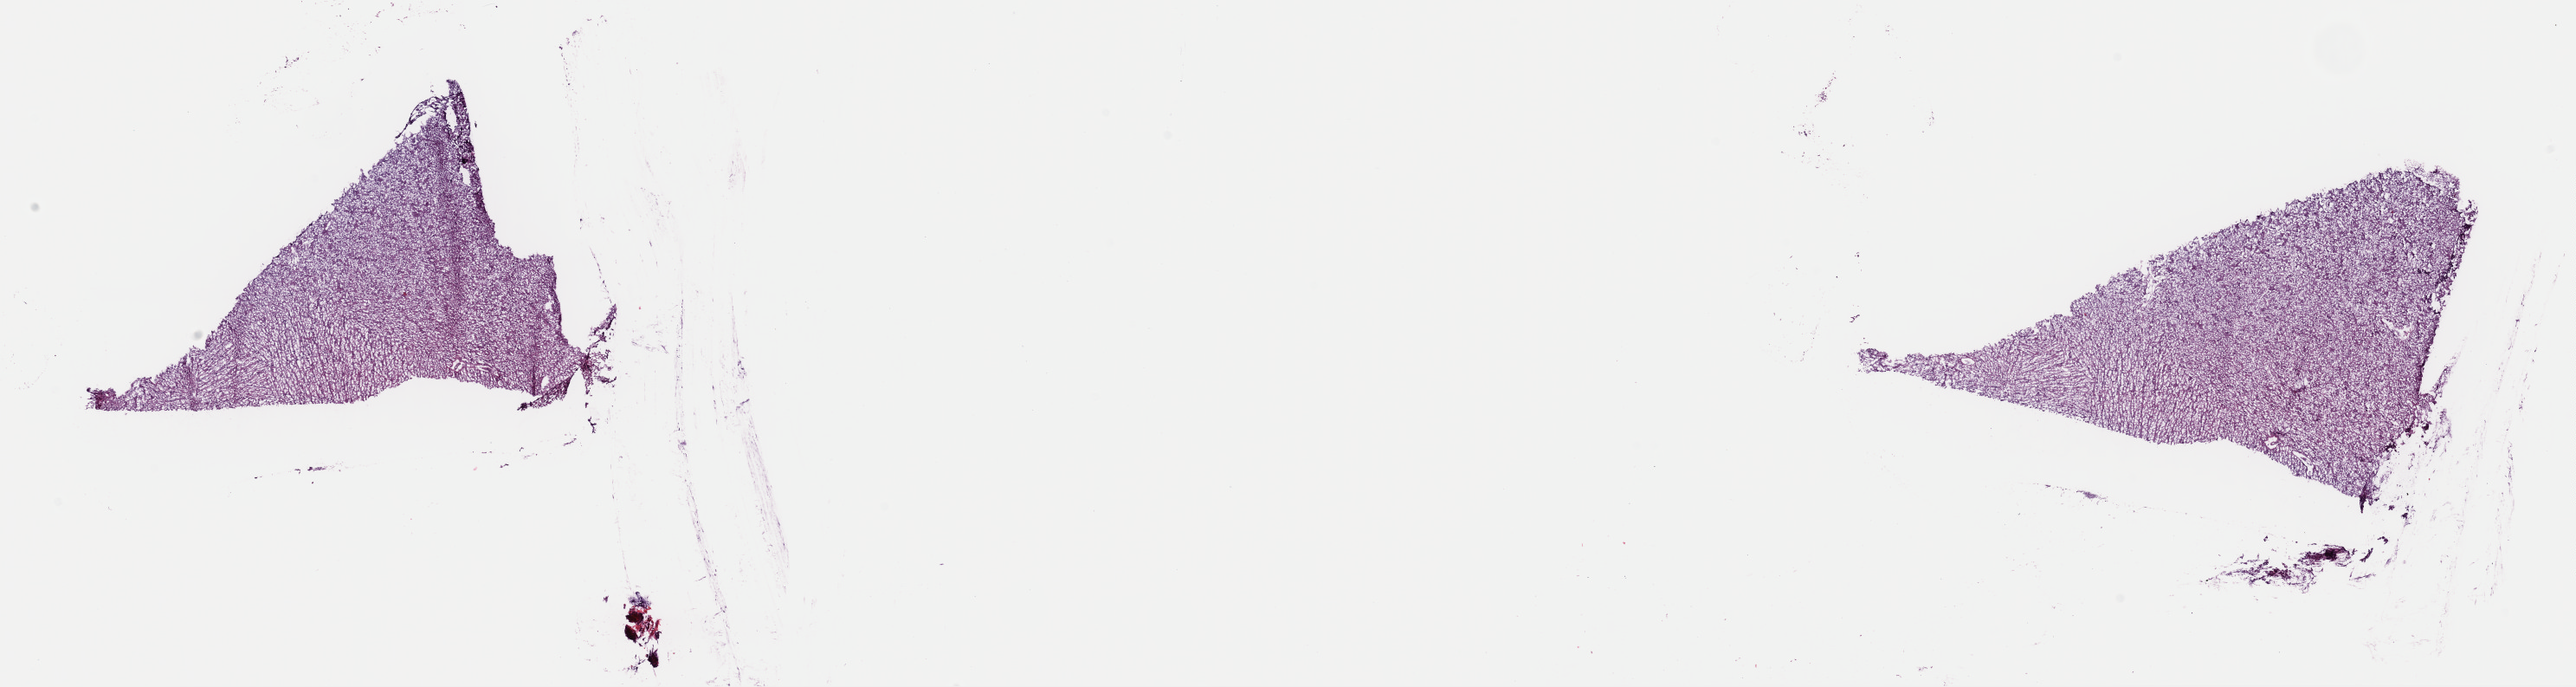
Whole-slide histology image, Hematoxylin and eosin (H&E) stained, low-resolution overview of the scanned area, about 23.5 x 6.3 mm, frozen section, primary tumour sample from the brain. Patient: female, age at initial diagnosis 45 years. Histologic grade: G2 (moderately differentiated). Pathologist review of this section (percent, as recorded): tumour cells 50%, tumour nuclei 80%, normal cells 10%, stromal cells 40%, necrosis 0%. Infiltration values recorded for this section: lymphocyte infiltration 0%, monocyte infiltration 0%, neutrophil infiltration 0%.
• laterality: left
• pathologic diagnosis: Mixed glioma (cerebrum)